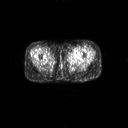
FDG PET of an extremity soft-tissue mass (from a PET/CT study), one axial slice; slice 8 of 267 in the series (ordered by position); 3.27 mm slice thickness; 128 × 128 image matrix. Female patient, age 47 years. From the clinical record (not read from this slice): histological type: myxofibrosarcoma; grade: intermediate; site of the primary tumour: left thigh.
Annotated regions visible in this slice (expert contour drawn on MRI and transferred to this co-registered scan by the dataset authors):
- gross tumour volume including surrounding oedema: bounding box (x1, y1, x2, y2) in pixels: (68, 53, 81, 61)